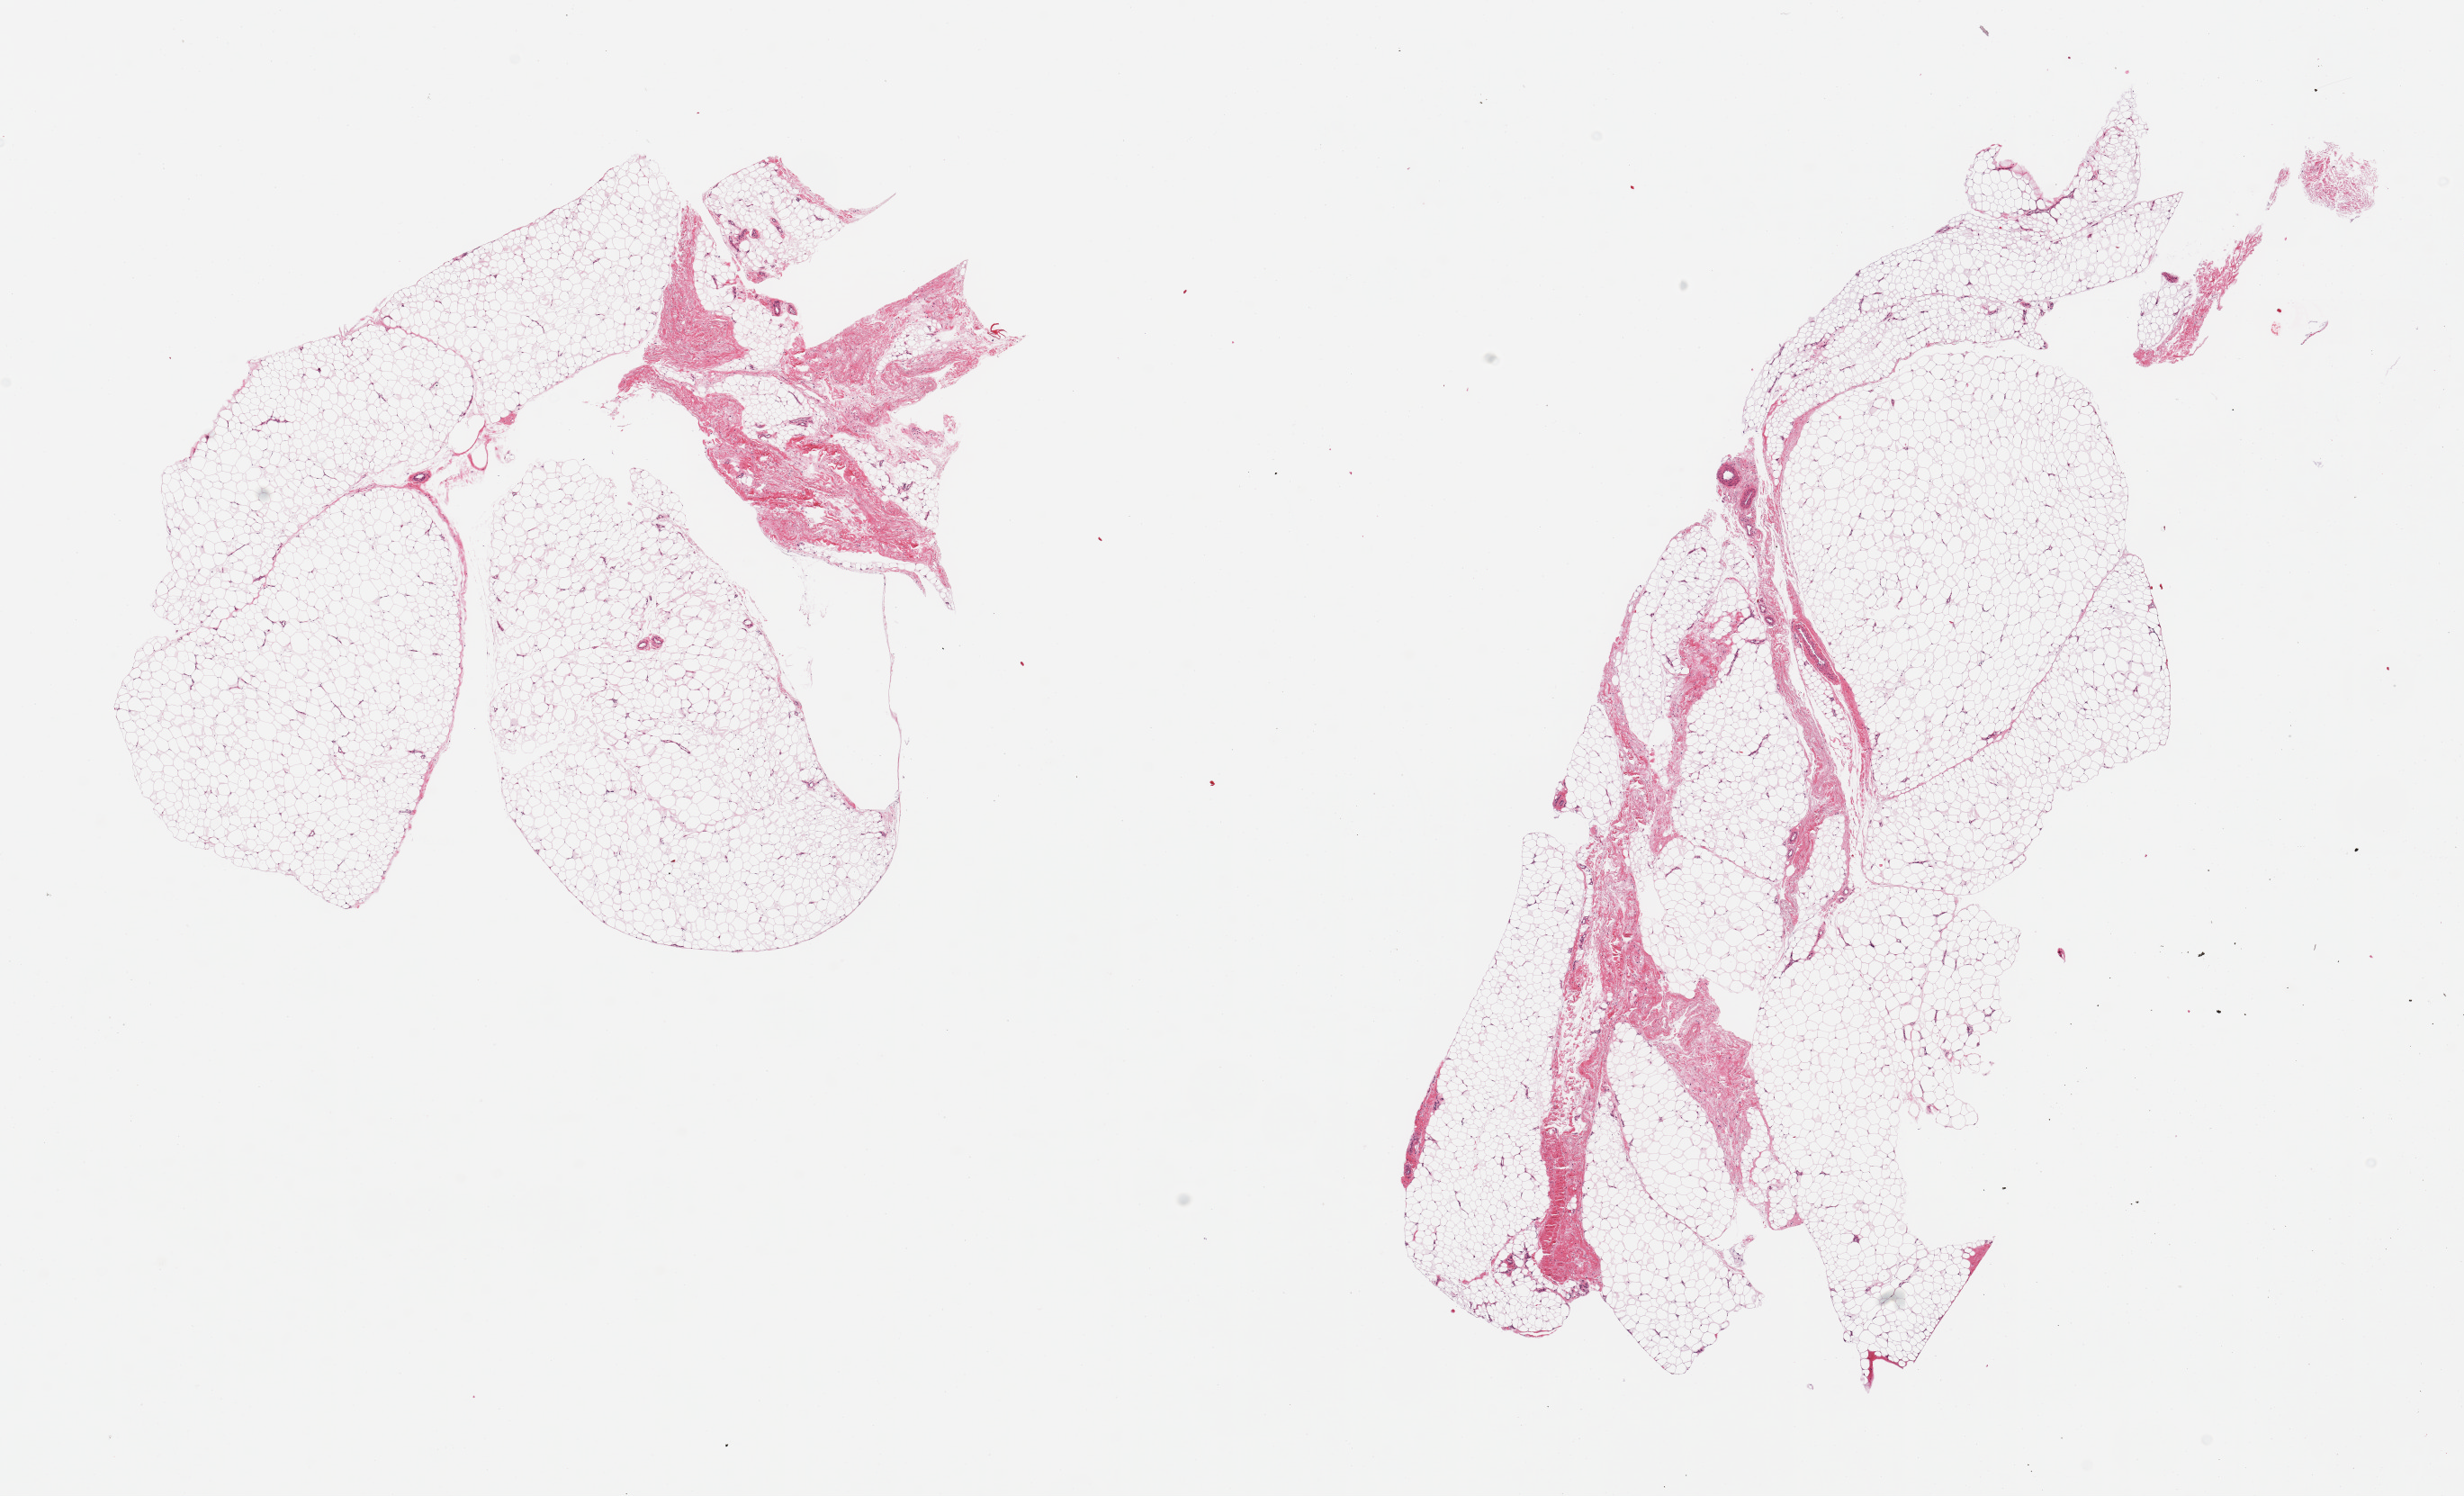
Whole-slide image, hematoxylin and eosin (H&E) stain, a low-resolution overview of the entire scanned area, about 21.7 x 13.1 mm (acquisition: 20x scan). PAXgene-fixed paraffin-embedded (PFPE) section. Target tissue: adipose tissue. Donor tissue sample. Male donor.
Pathologist's review note for this sample: 2 pieces; 10% fibrous content.